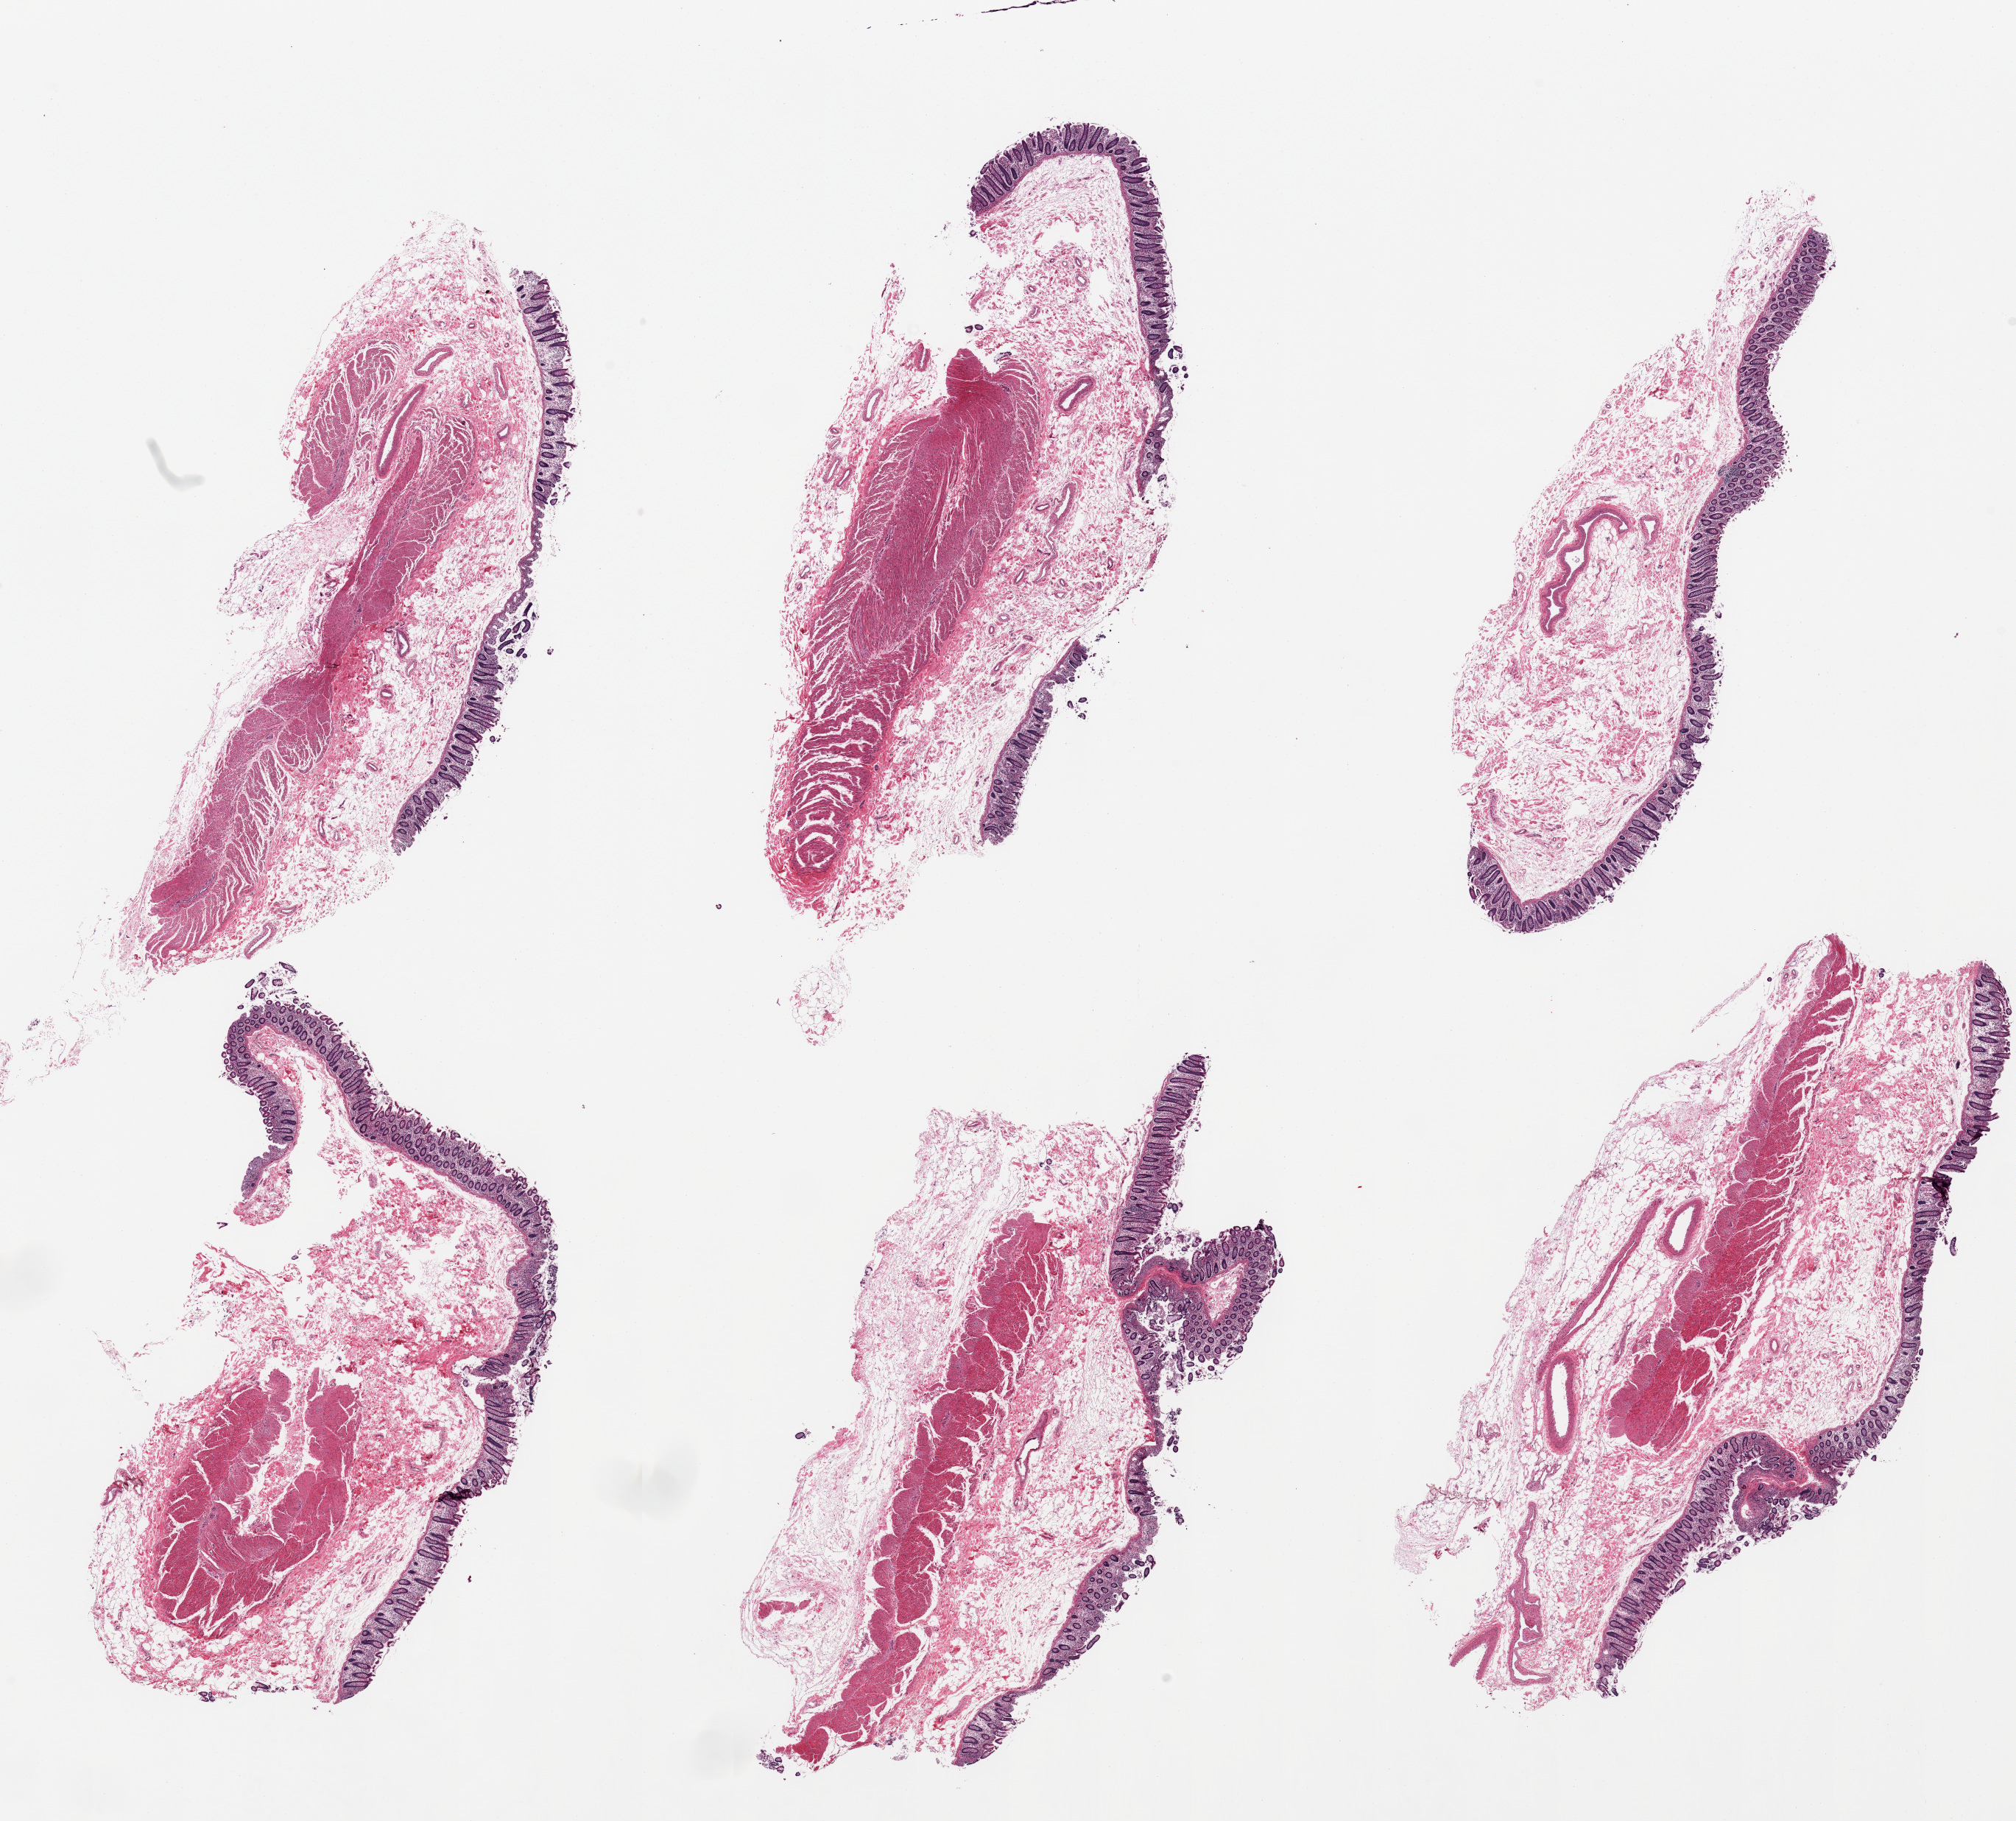
Digitized hematoxylin and eosin (H&E)-stained section — low-resolution overview of the scanned area, about 21.7 x 19.6 mm (from a 20x scan). PAXgene-fixed, paraffin-embedded tissue. Section of transverse colon (target tissue). Donor tissue sample. Donor sex: male.
* pathologist's review note for this sample: 6 pieces; 1 piece has no muscularis